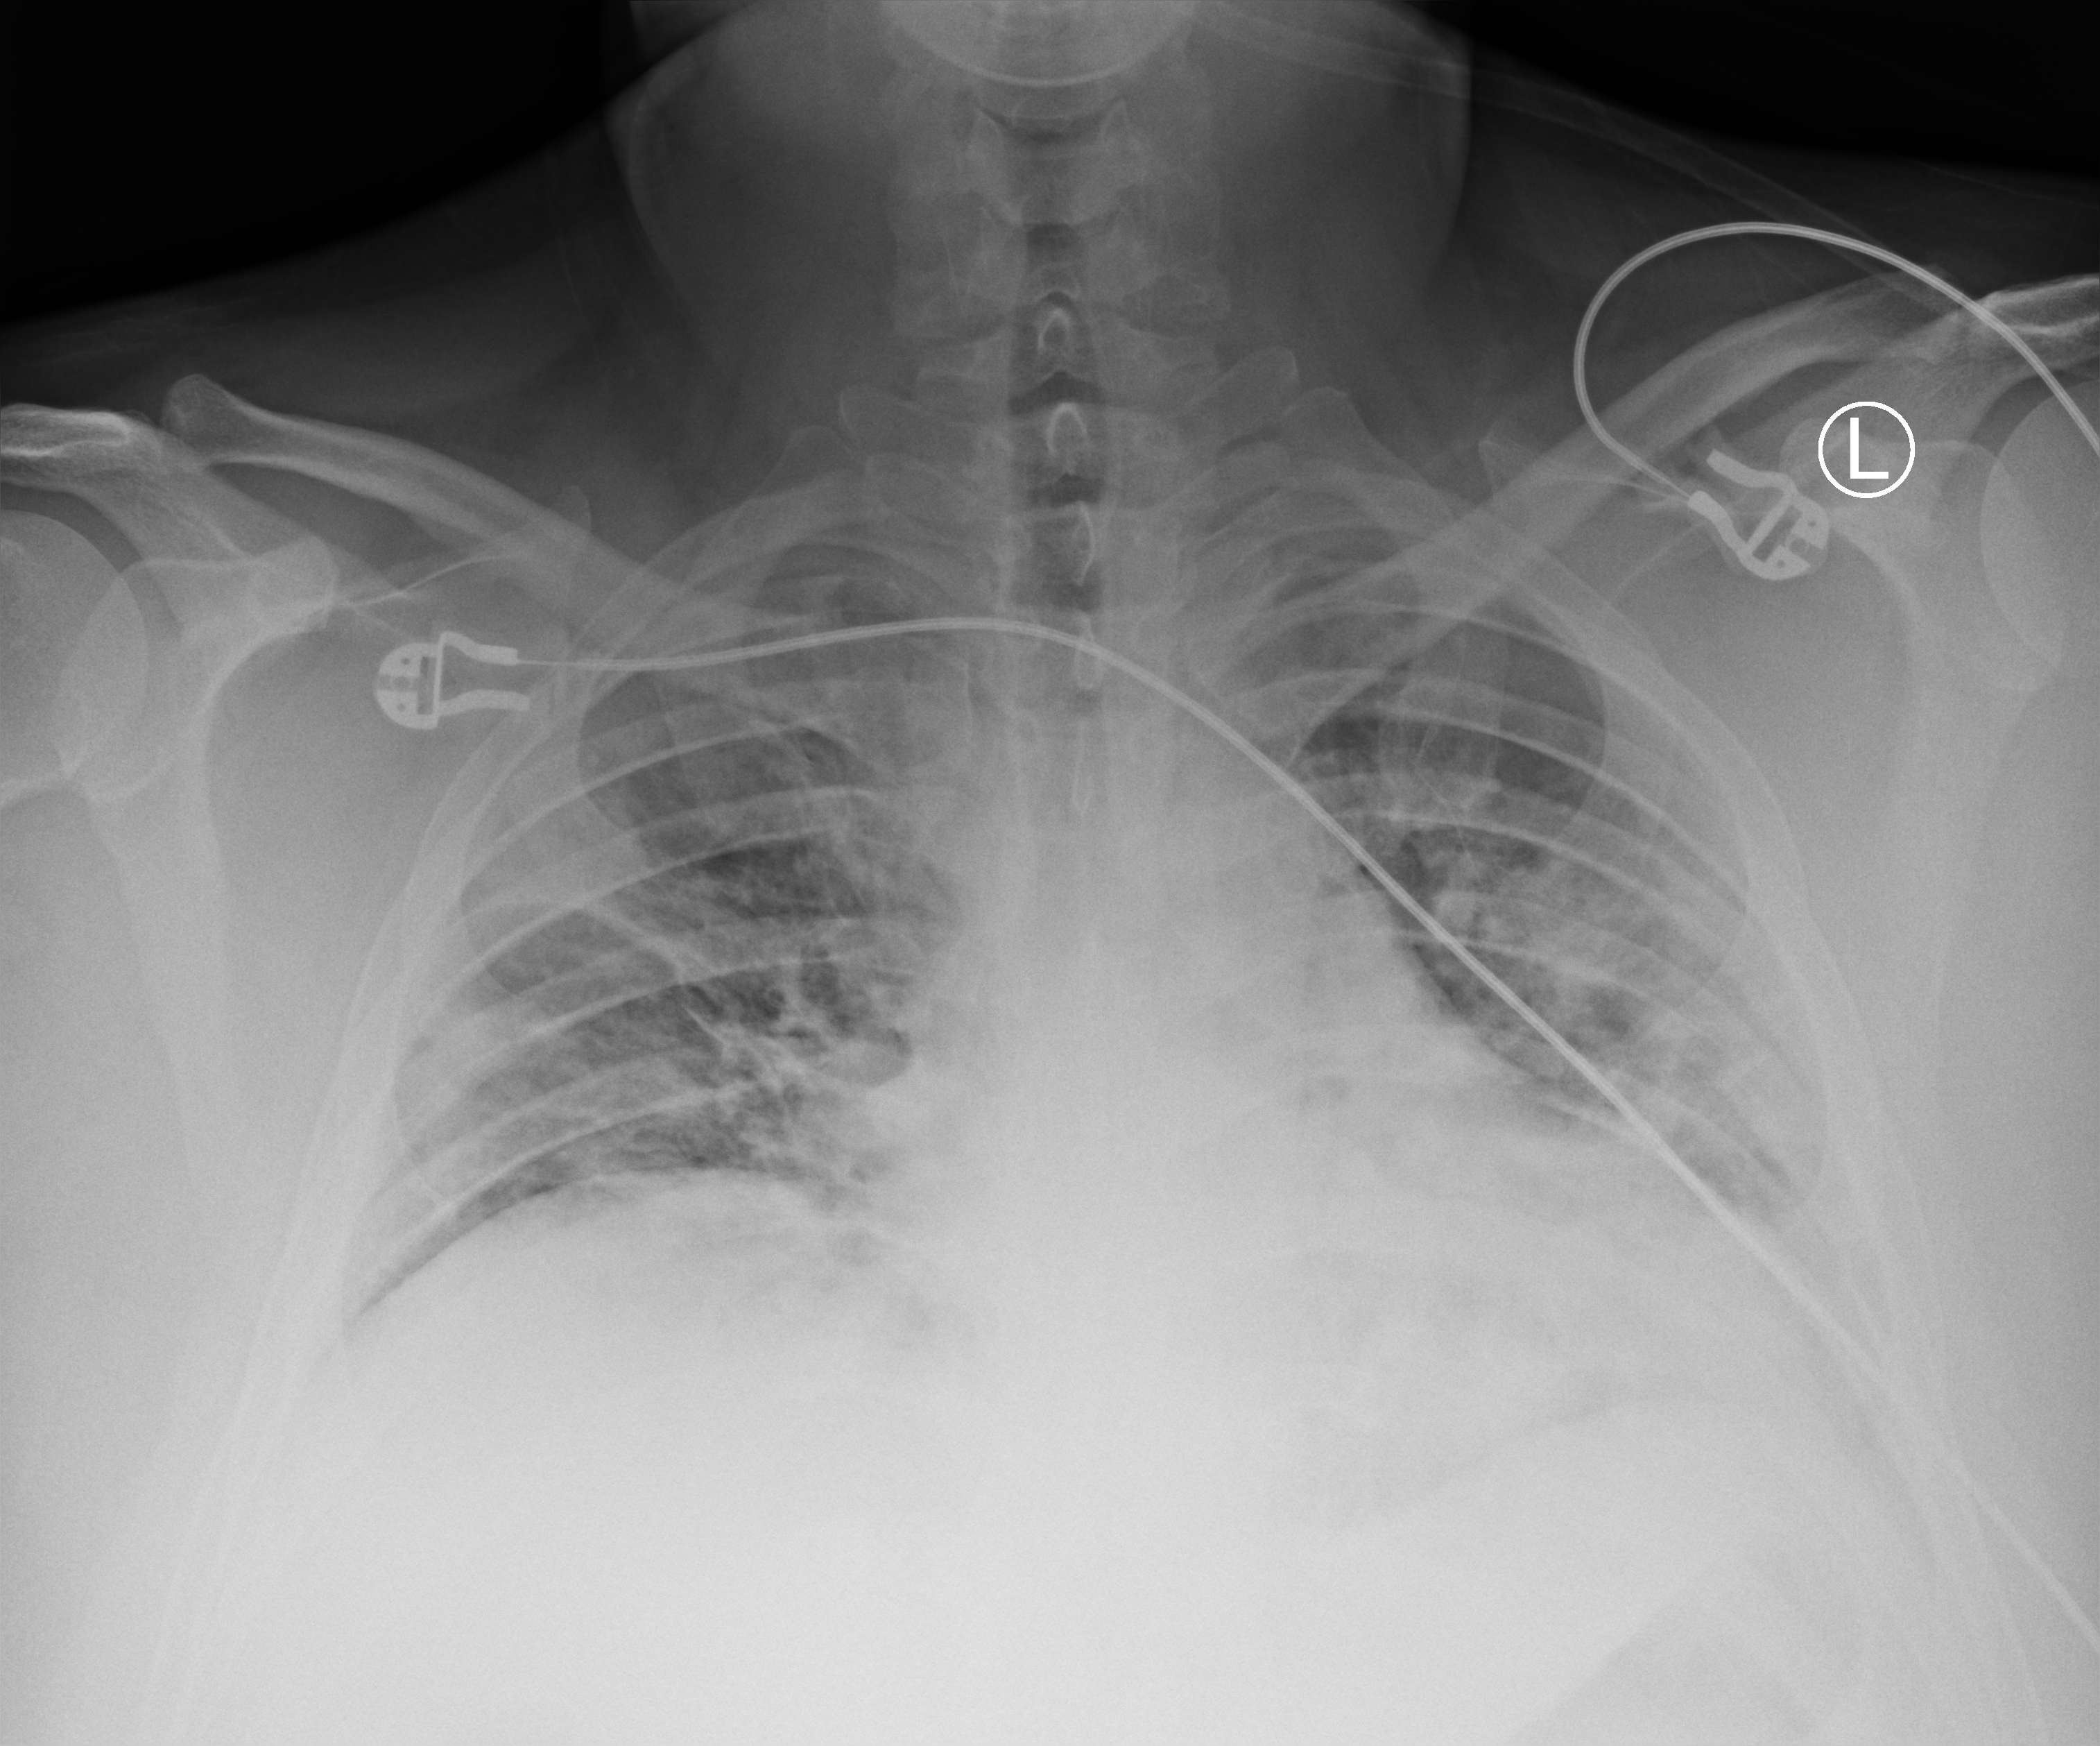
Bedside chest radiograph (computed radiography), anteroposterior (AP) projection. Male patient hospitalised with COVID-19, age 18–59 years.
Hospital-stay facts (about this admission, not read from this image; timing relative to this image not recorded): smoking status (admission record): never.